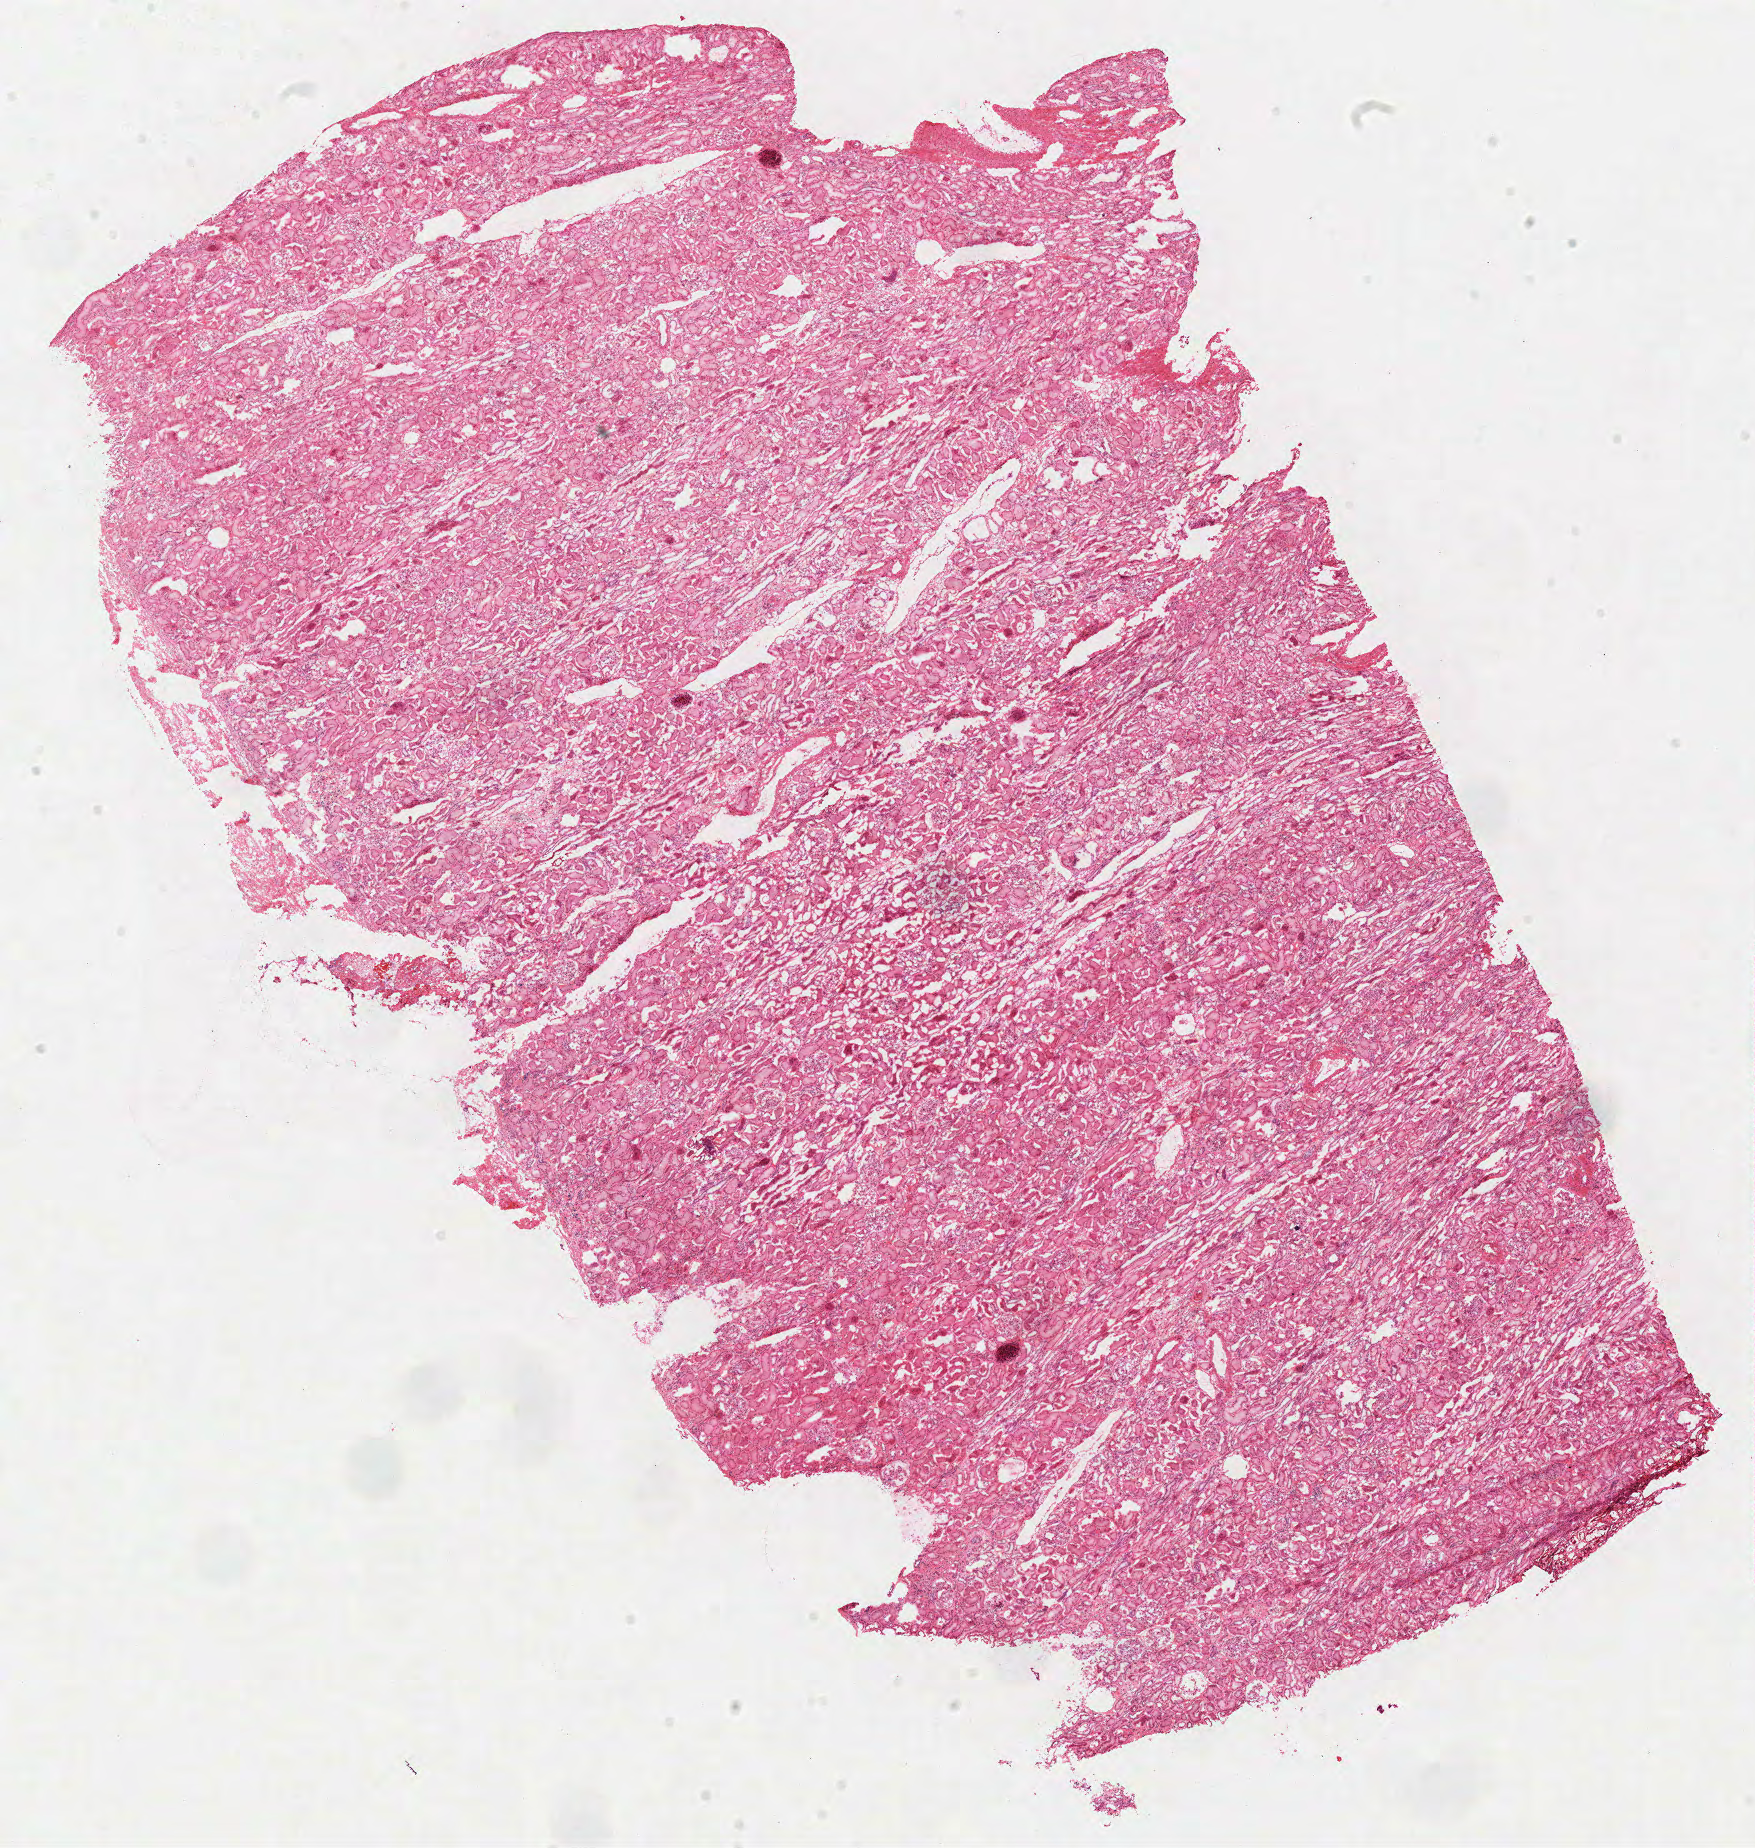
Whole-slide histology image, H&E-stained, a low-resolution overview of the entire scanned area, about 13.8 x 14.6 mm (slide scanned at 40x); frozen section from the top of the tissue portion; solid tissue normal (non-tumour tissue) sample from the kidney. Male, age 61 years at initial diagnosis.
This section: solid tissue normal (non-tumour) sample from the same patient. Patient diagnosis: Papillary adenocarcinoma, NOS.